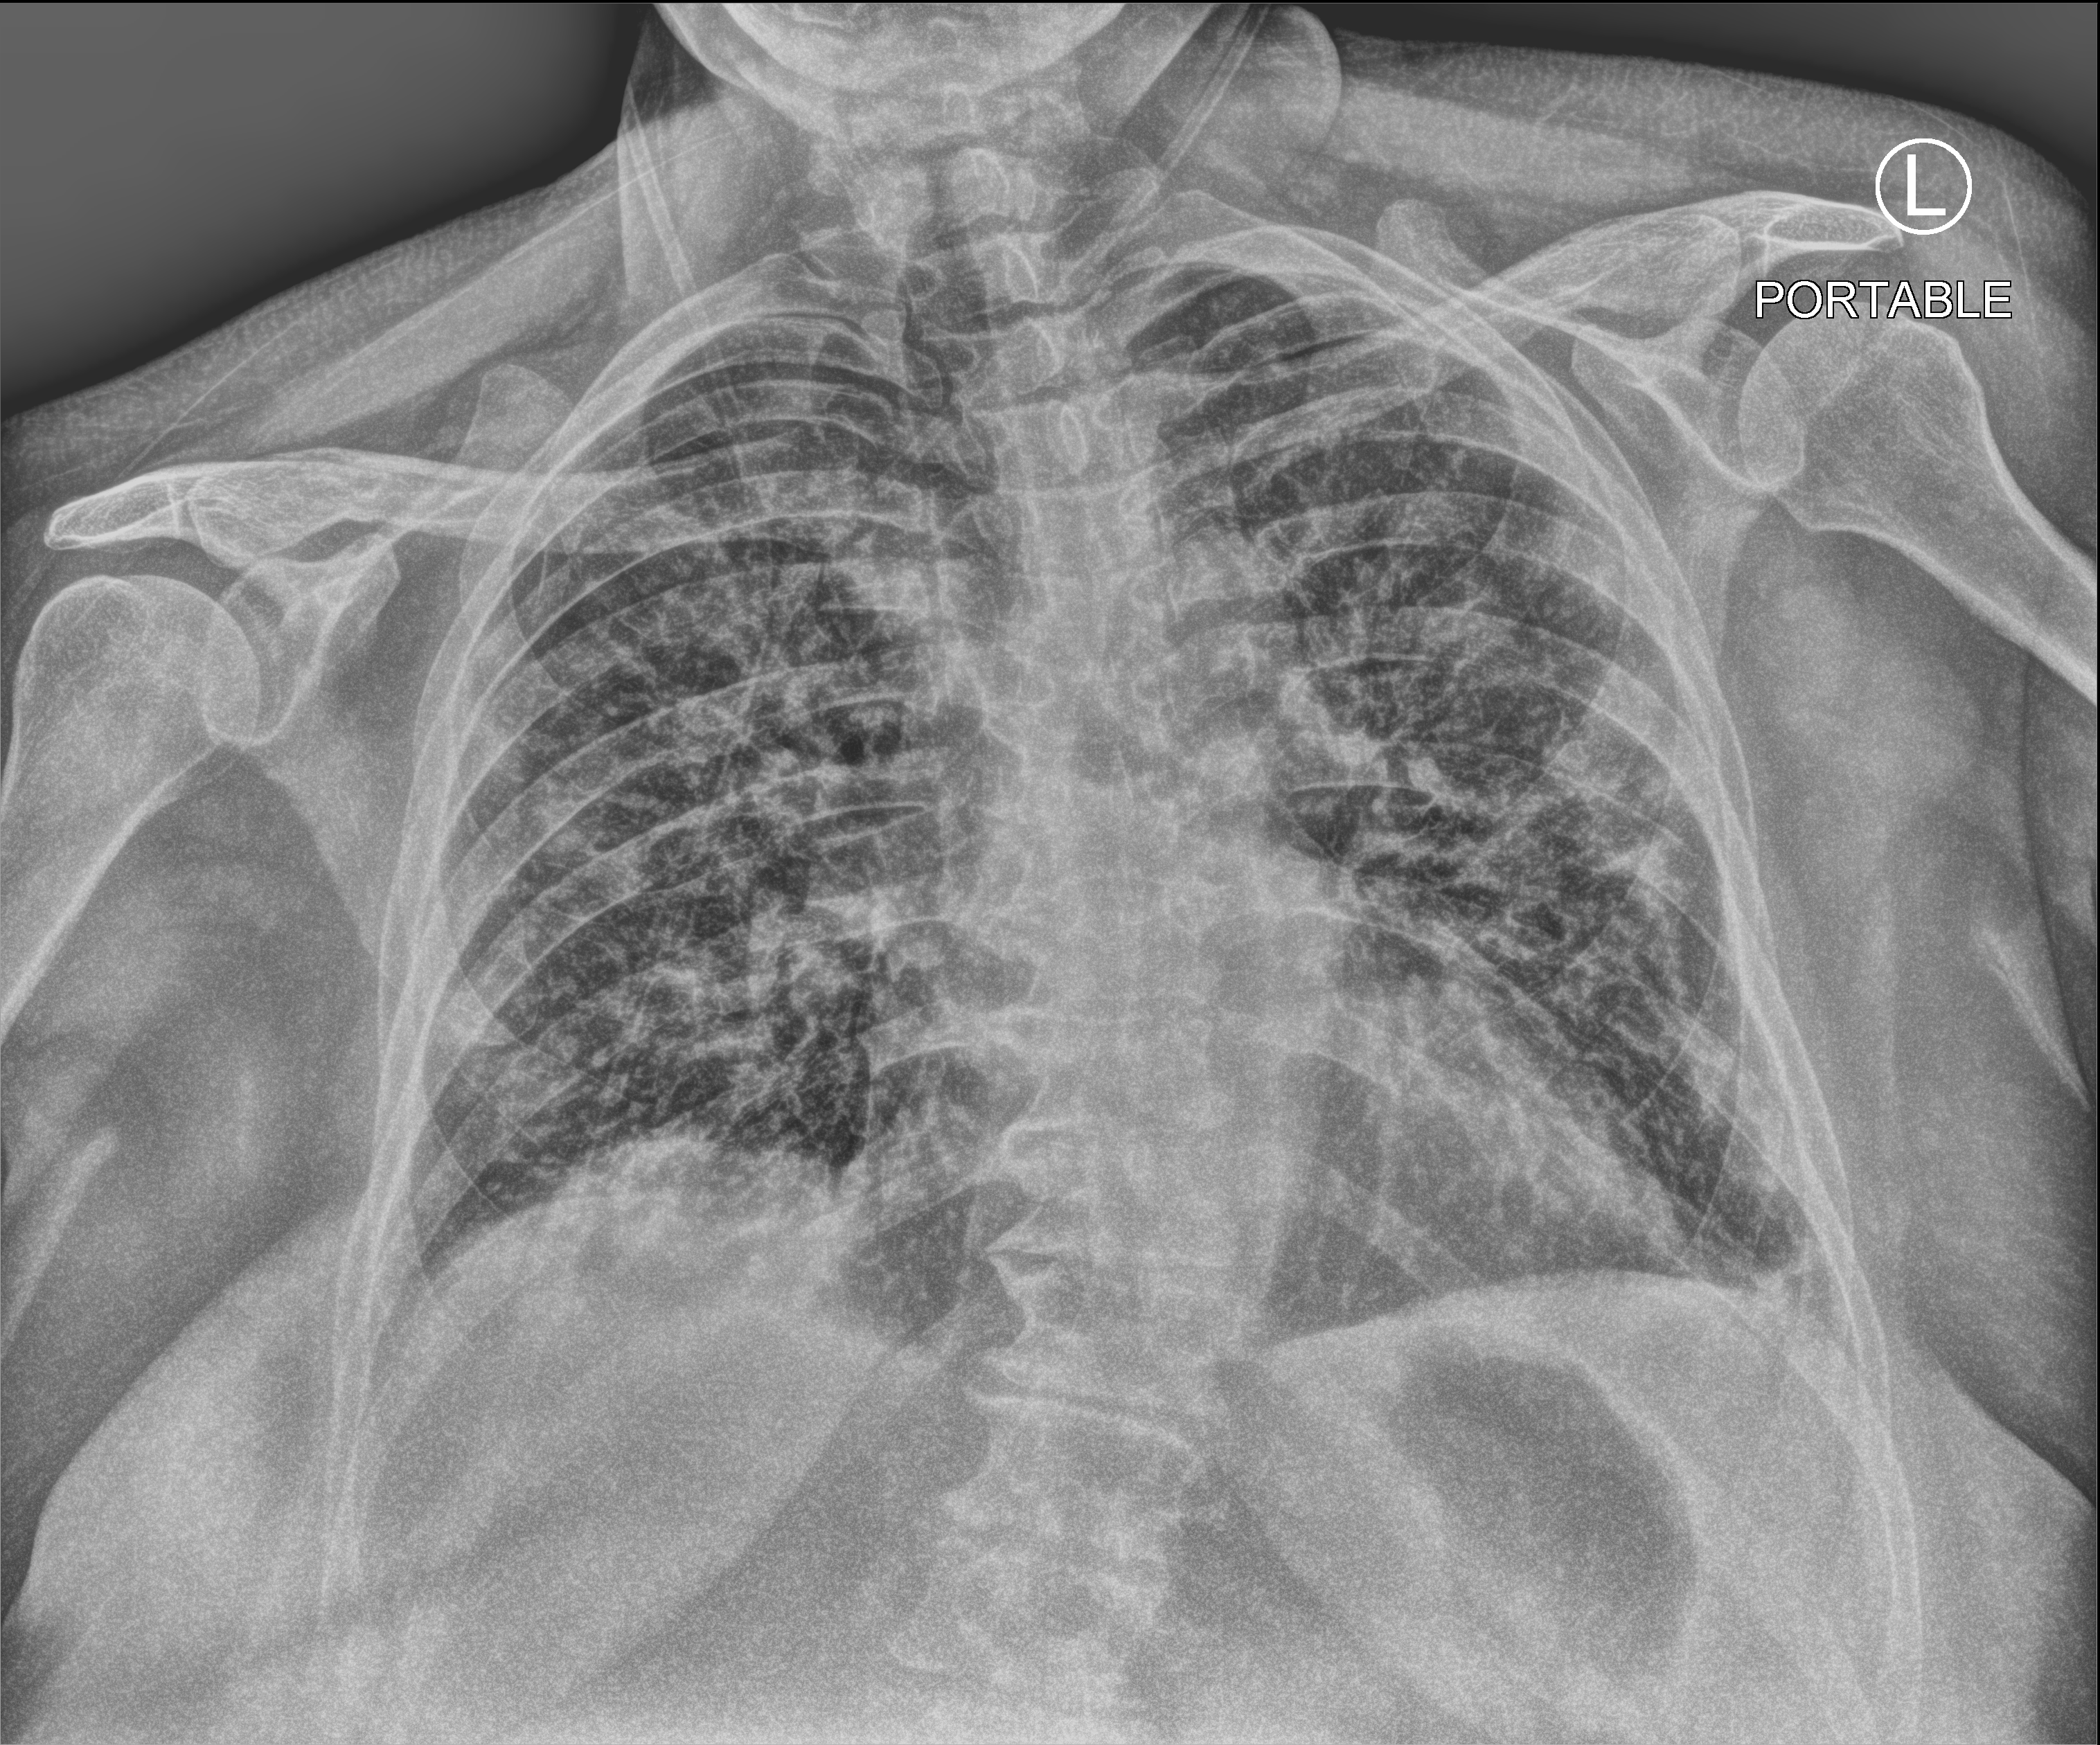
Portable chest radiograph; anteroposterior (AP) projection. Female patient hospitalised with COVID-19, age 60–74 years.
From the hospital-stay record, not from the radiograph (when in the stay this image was taken is not recorded): length of hospital stay: 7 days; mechanically ventilated during this hospital stay: no.